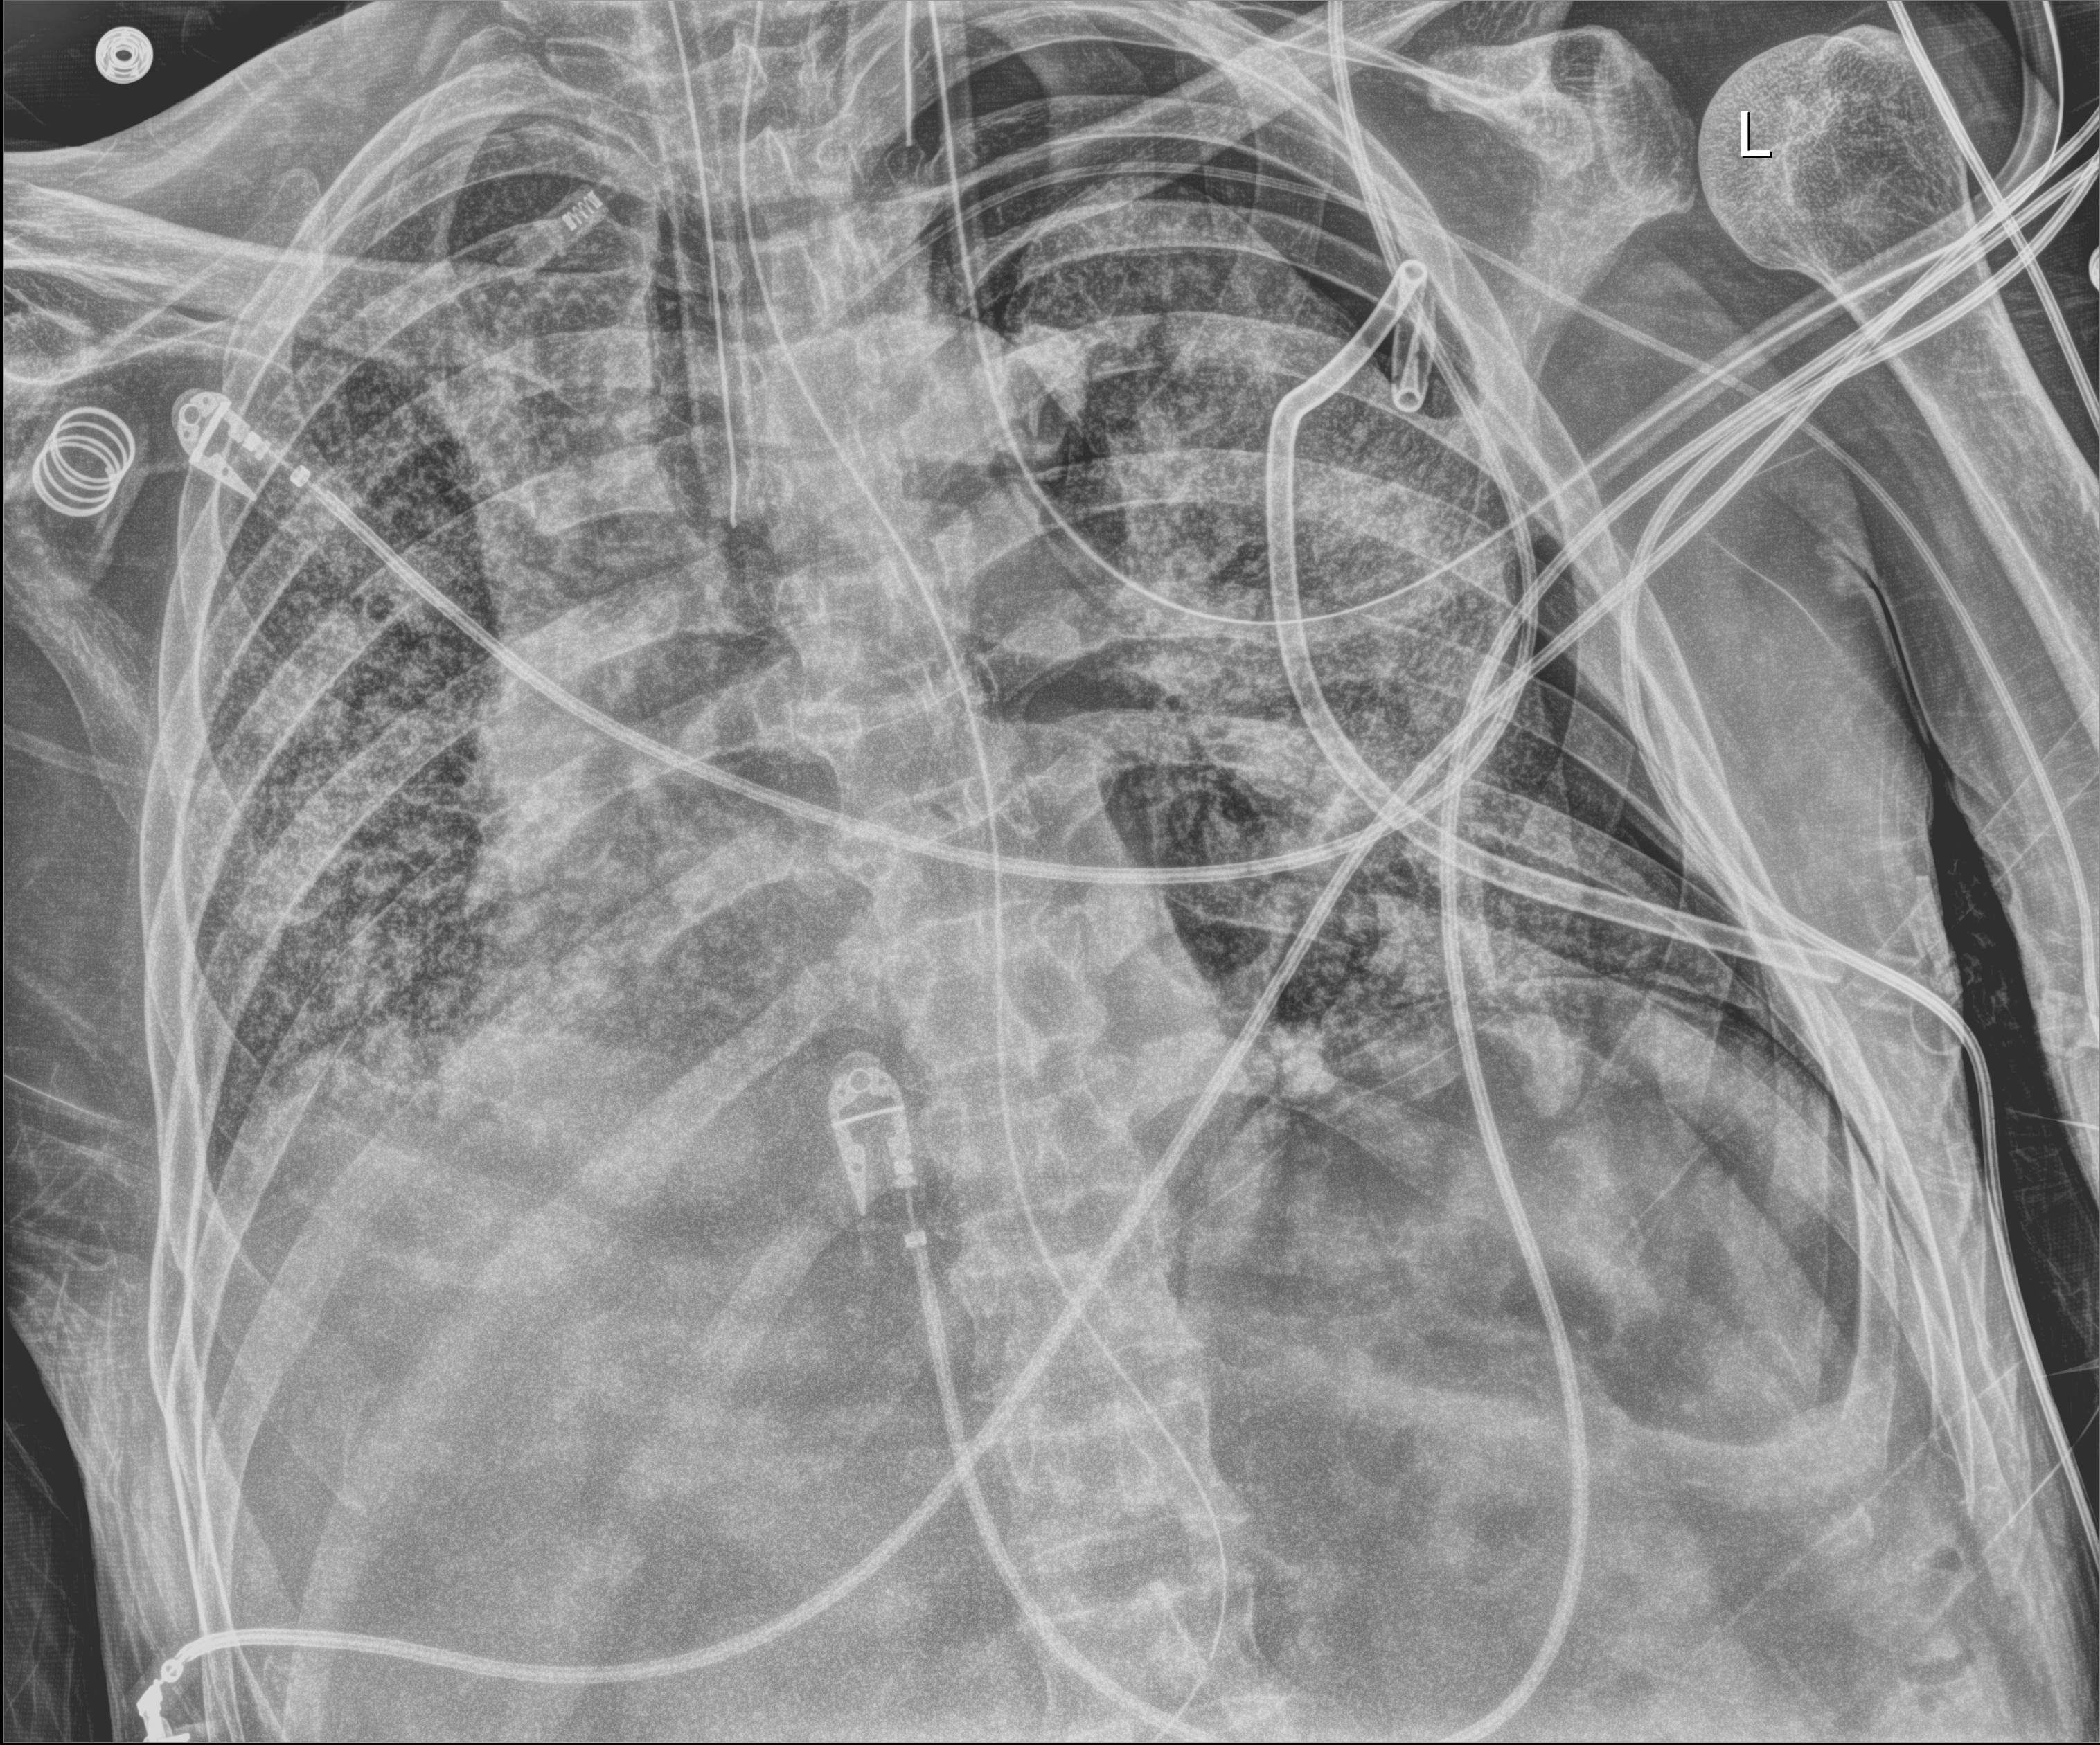
Bedside chest radiograph (digital radiography); anteroposterior (AP) projection. Patient hospitalised with COVID-19; male, aged 60–74 years.
Hospital-stay facts (about this admission, not read from this image; timing relative to this image not recorded): admitted to intensive care during this hospital stay: yes; length of hospital stay: 54 days; mechanically ventilated during this hospital stay: yes.